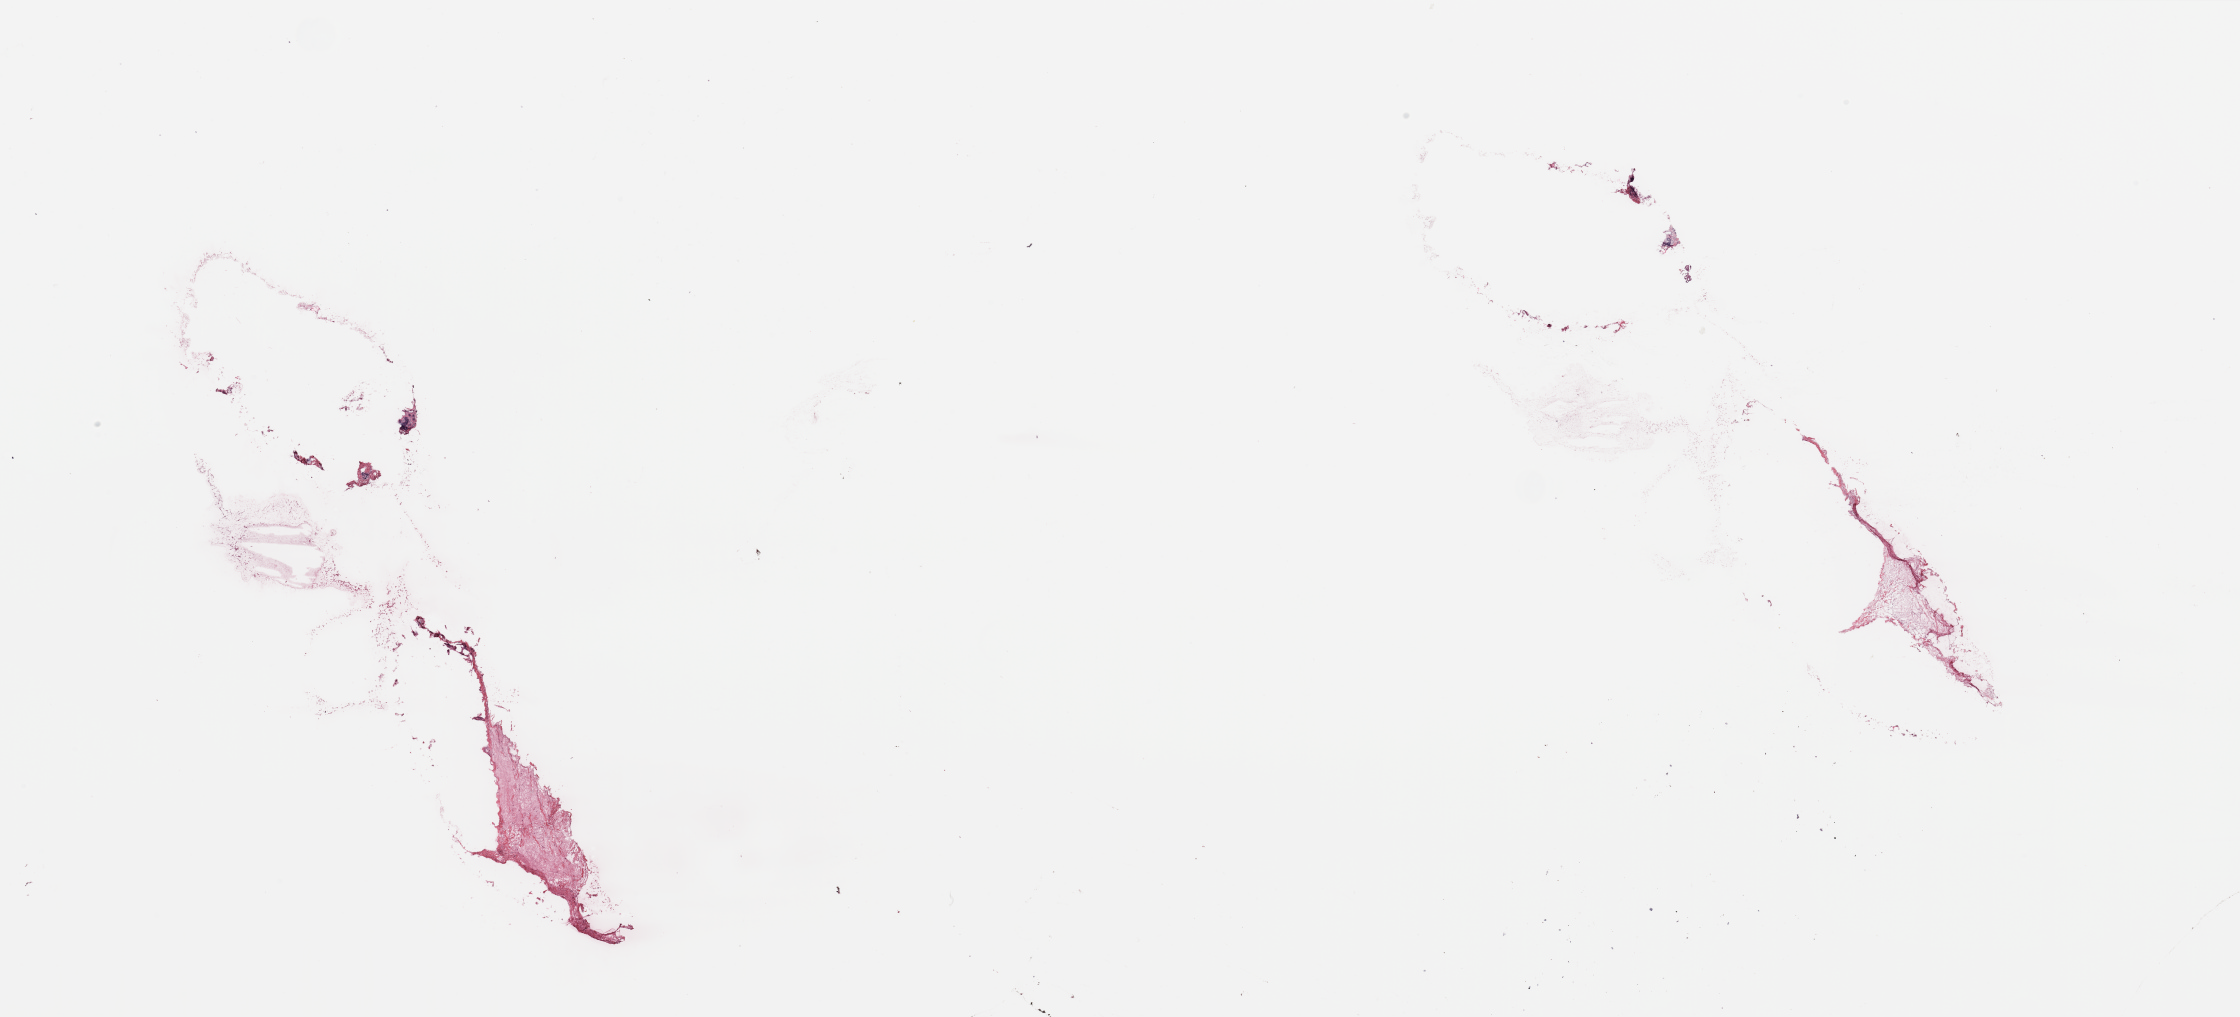
H&E-stained whole-slide image — shown as a low-resolution overview of the whole scanned area (about 35.4 x 16.1 mm, acquisition: 20x scan); breast, tissue type not recorded.
Patient diagnosis (cohort enrolment): breast cancer (breast).